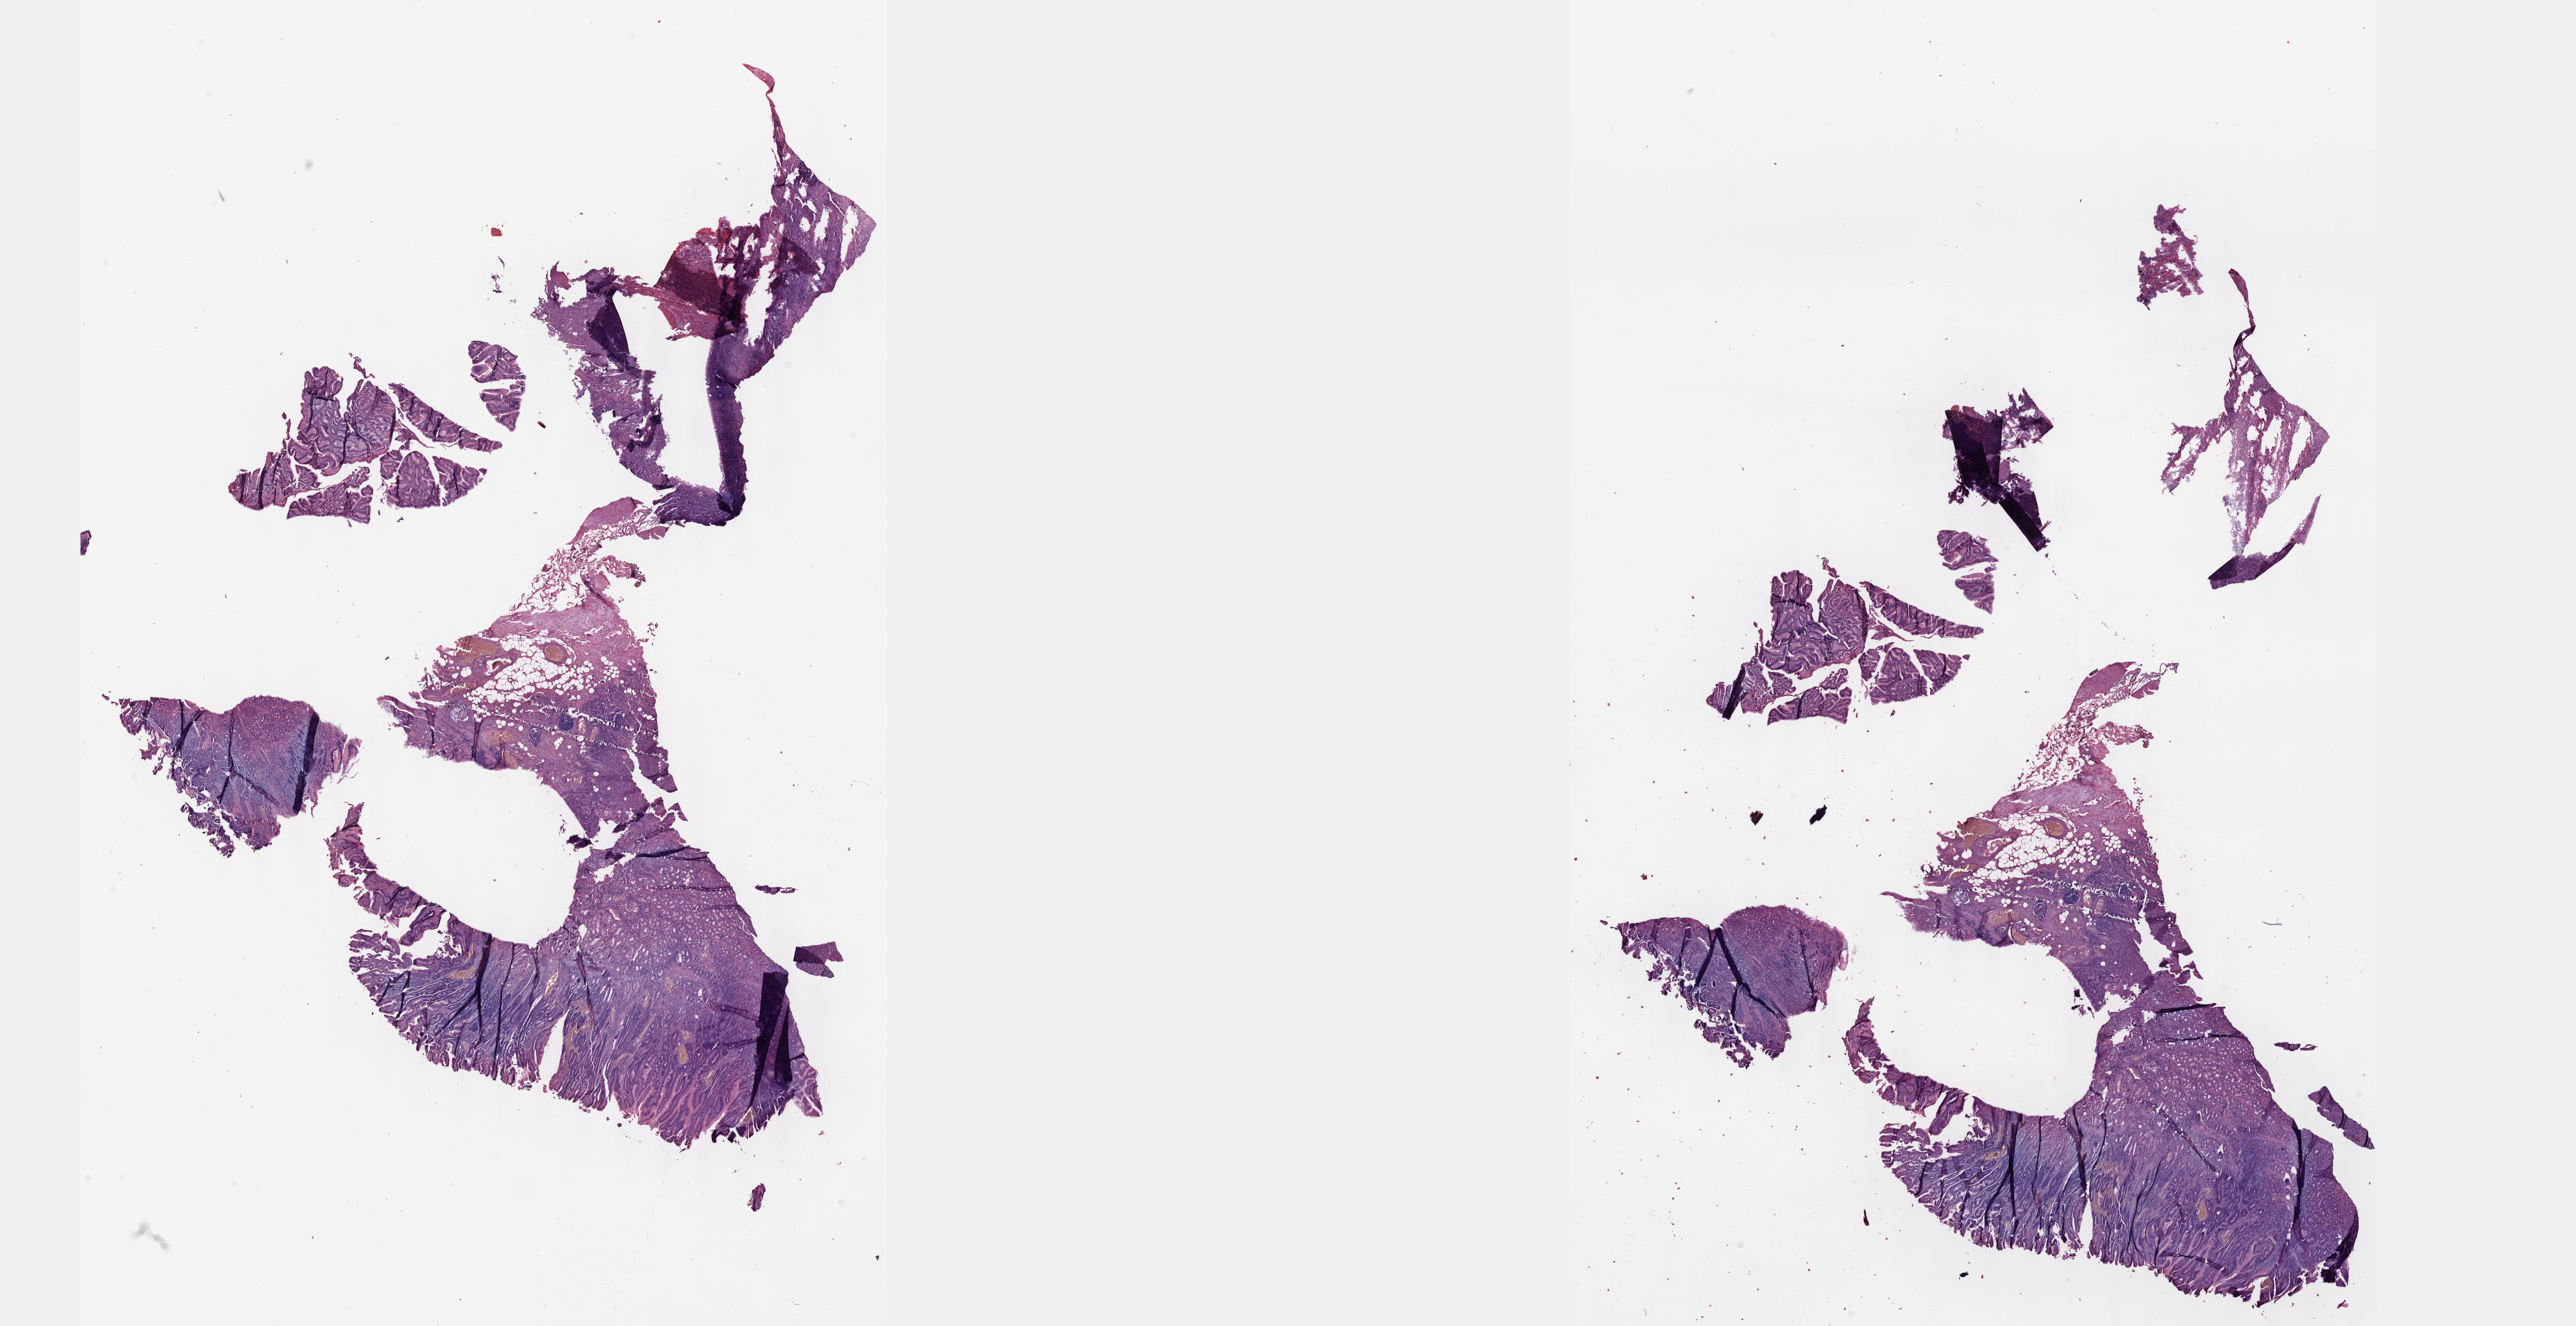
Digitized Hematoxylin and eosin (H&E) stained tissue section (whole slide) — low-resolution overview of the scanned area, about 32.2 x 16.6 mm (slide scanned at 40x), formalin-fixed paraffin-embedded (FFPE) diagnostic section, stomach, primary tumour sample. Male, age 57 years at initial diagnosis. Histologic grade: GX (grade cannot be assessed).
* diagnosis: Signet ring cell carcinoma (body of stomach)